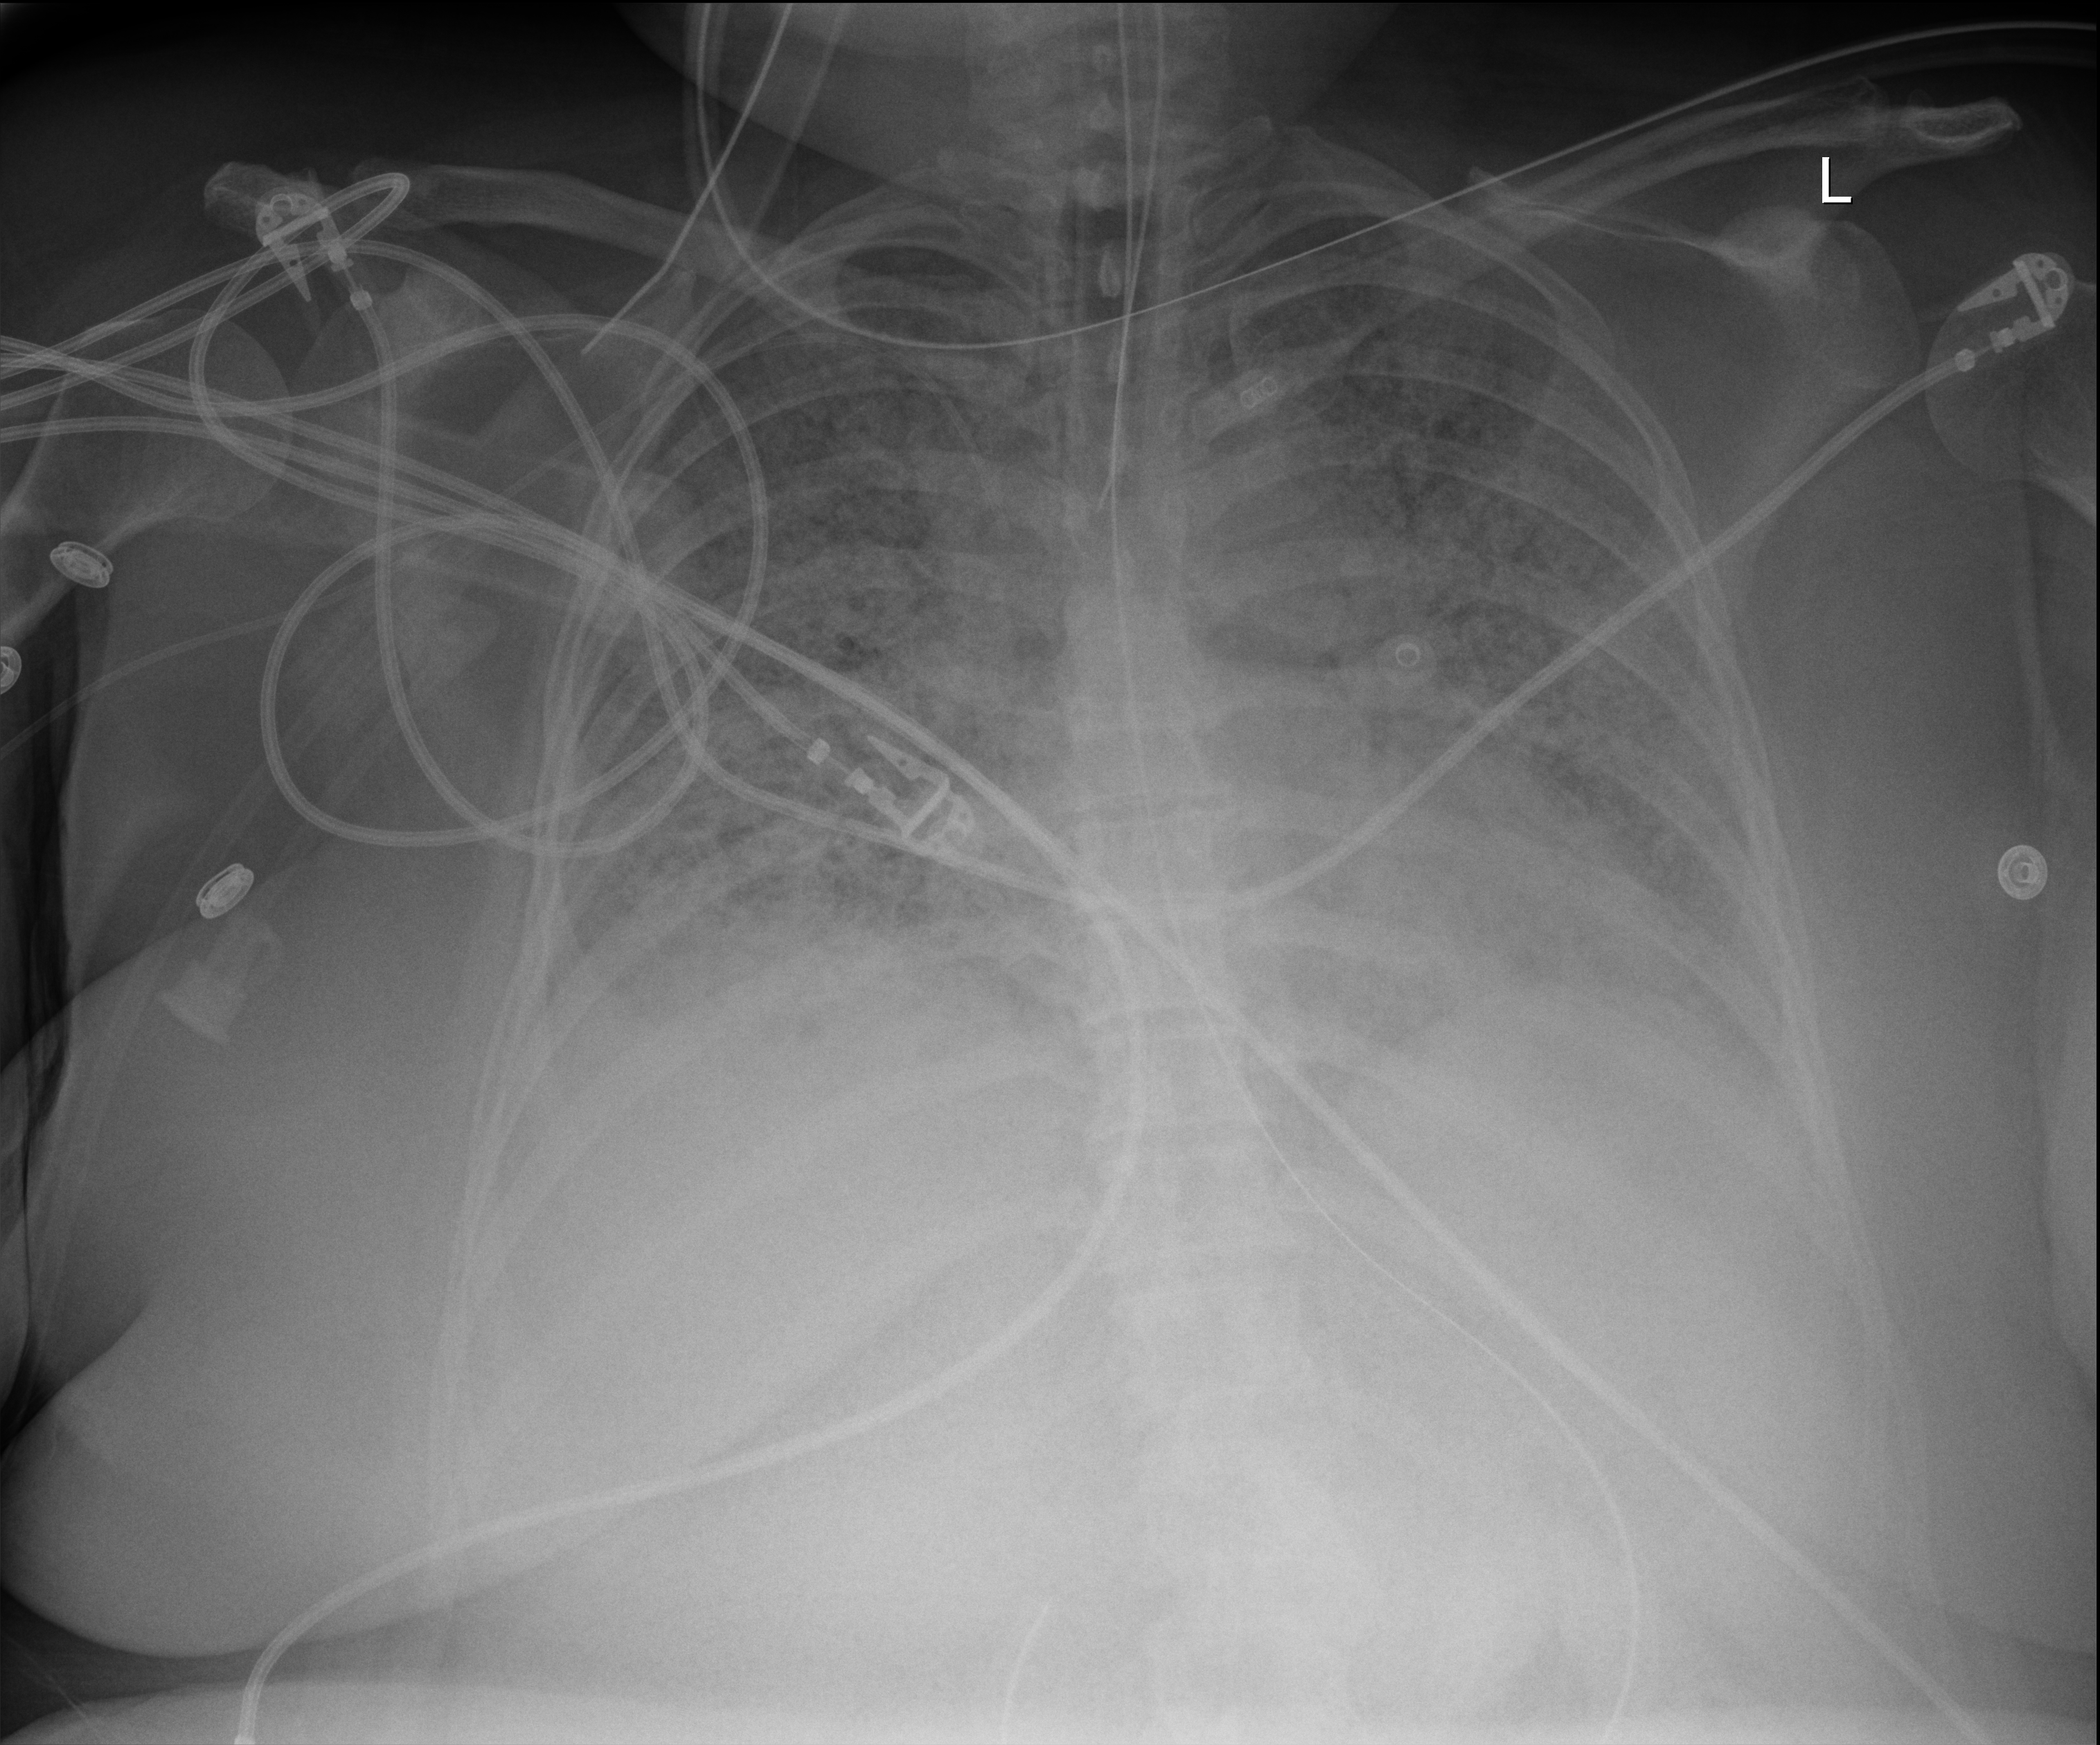
Portable chest radiograph; anteroposterior (AP) projection. Female patient hospitalised with COVID-19, age 18–59 years.
From the hospital-stay record, not from the radiograph (when in the stay this image was taken is not recorded): diabetes (admission record): no.